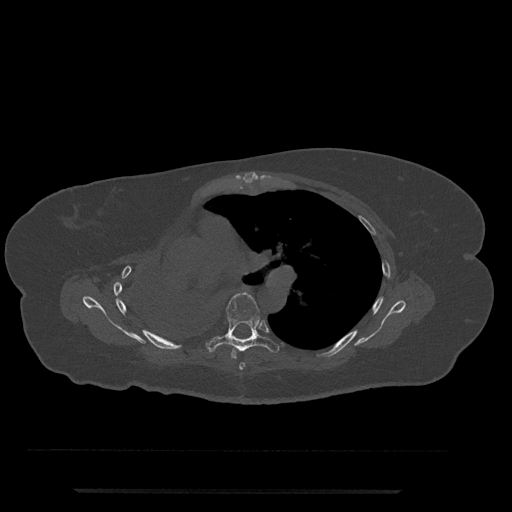
CT including the spine, one axial slice; slice 501 of 797 in the series (ordered by position); reconstruction kernel Br40s/3; 120 kVp; bone window (W 1800 / L 400 HU); 0.5 mm slice thickness; 512 × 512 image matrix, field of view 440 × 440 mm. Female patient, age 51 years. From the clinical record (not read from this slice): primary cancer: neuro; vertebrae with lytic lesions (as recorded): T8.
Structures marked on this image (semi-automatically segmented with operator editing):
- T5 vertebra: box from (x=239, y=362) to (x=246, y=370) px
- T6 vertebra: (x=206, y=293)–(x=279, y=359)